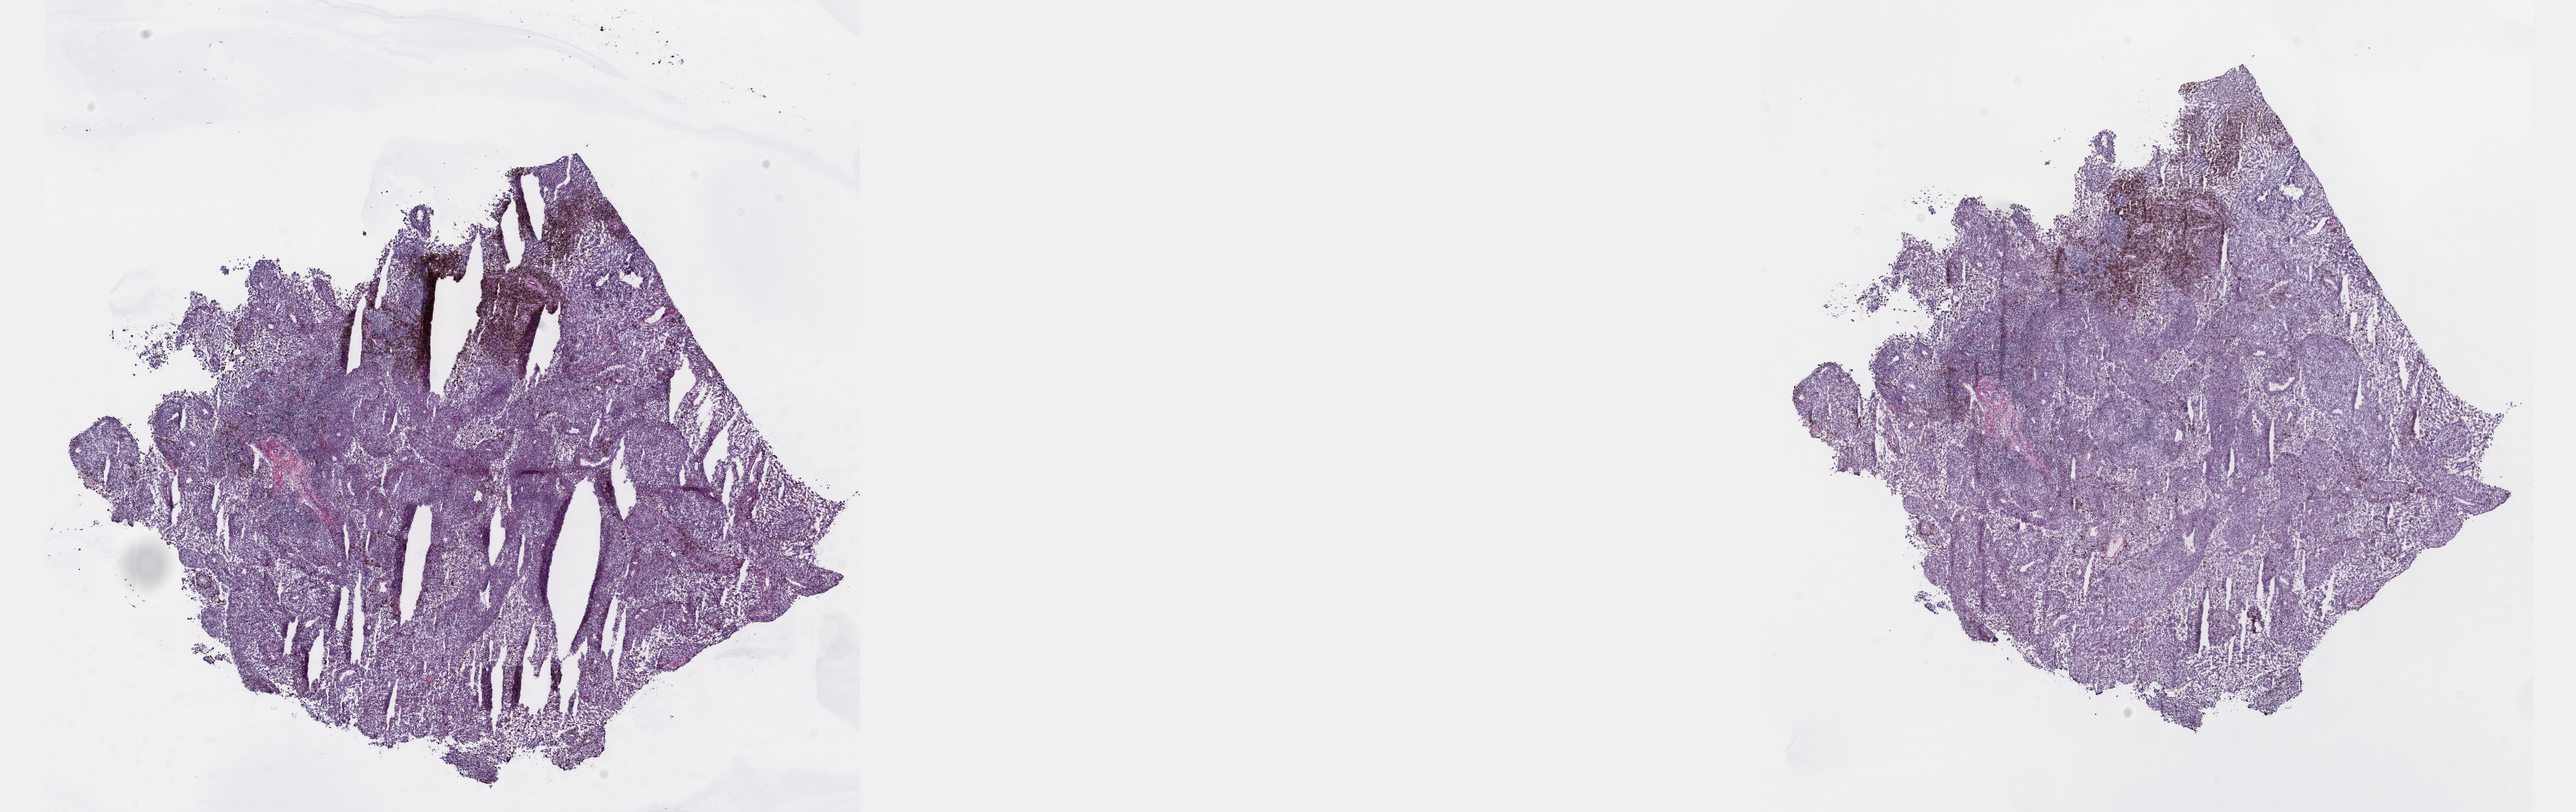
H&E whole-slide image — whole scanned area (about 28.7 x 9.0 mm, slide scanned at 40x) shown as a low-resolution overview; frozen section from the top of the tissue portion; metastatic tumour sample, sampled site: lymph nodes of axilla or arm. Female patient; age at initial diagnosis 57 years. Pathologist review of this section (percent, as recorded): tumour cells 70%, tumour nuclei 70%, normal cells 0%, stromal cells 30%, necrosis 0%. Inflammatory infiltration, as recorded: lymphocyte infiltration 10%, monocyte infiltration 5%, neutrophil infiltration 0%.
This section: metastatic tumour tissue. Patient diagnosis: Malignant melanoma, NOS.